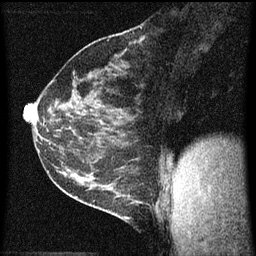
Breast MRI (dynamic contrast-enhanced), one sagittal slice; slice 27 of 60 in the series (ordered by position); dynamic contrast-enhanced series, image 2 of 3 at this slice position (ordered by acquisition); 1.5 T; TE 4.2 ms, TR 8 ms; 256 × 256 image matrix. Patient: female, 35 years.
Outlined on this slice (semi-automatically segmented with operator editing):
- analysis volume of interest (the breast-tissue region the enhancement analysis was run in; not a lesion): bounding box <106,182,149,223> (left, top, right, bottom; pixels)
- tumour enhancement mask (voxels above the 70 % enhancement threshold inside the analysis volume of interest): <124,194,129,219>